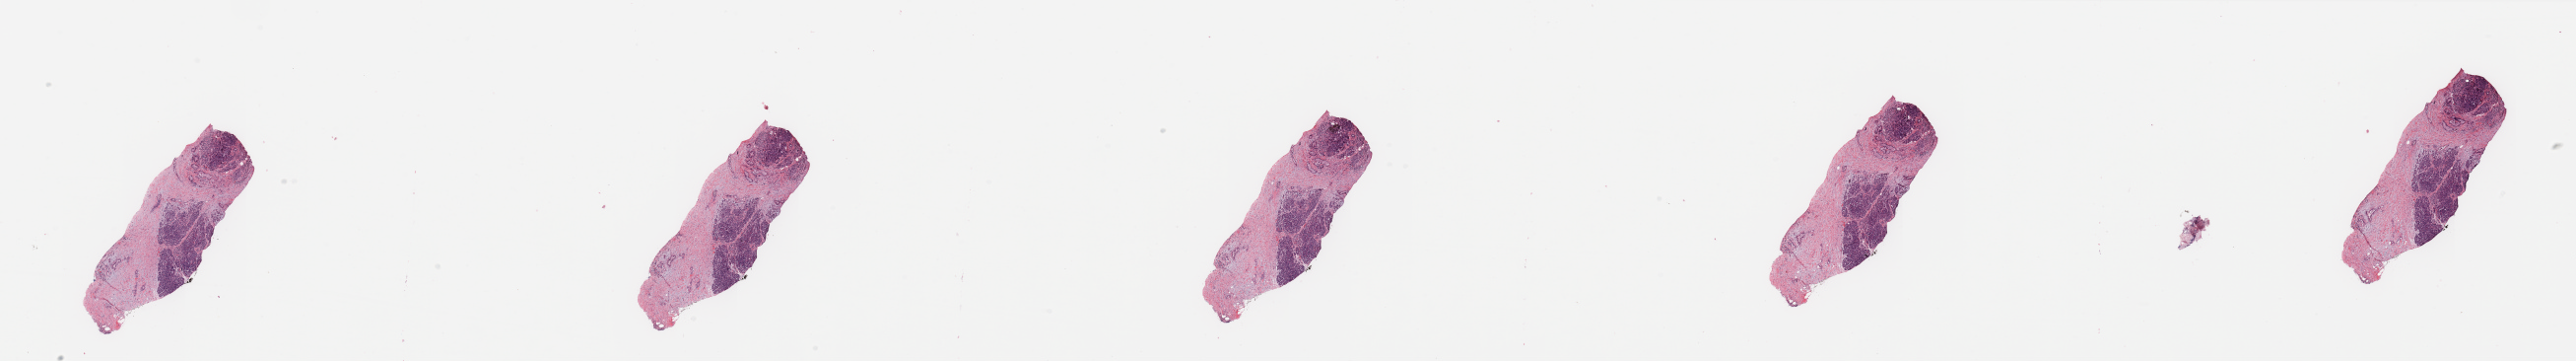
Whole-slide histology image, Hematoxylin and eosin (H&E) stained, low-resolution overview of the scanned area, about 41.3 x 5.8 mm (from a 20x scan); tumour tissue sample, pancreas. Patient: male, age 74 years. Histologic grade: G1 (well differentiated).
- diagnosis: Infiltrating duct carcinoma, NOS
- AJCC pathologic stage: IB